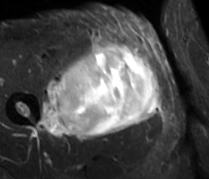
MRI of an extremity soft-tissue mass, one axial slice; slice 40 of 89 in the series (ordered by position); STIR; MR volume resampled by the dataset authors to the PET/CT grid (not the native acquisition matrix); 3.27 mm slice thickness; 209 × 179 image matrix, field of view 204 × 175 mm. Male patient. From the clinical record (not read from this slice): histological type: undifferentiated - pleiomorphic; grade: high; site of the primary tumour: right thigh.
Outlined on this slice (expert contour drawn on MRI and transferred to this co-registered scan by the dataset authors):
- gross tumour volume including surrounding oedema: bounding box (x1, y1, x2, y2) in pixels: (39, 41, 161, 138)
- gross tumour volume (mass): (57, 44, 159, 138)